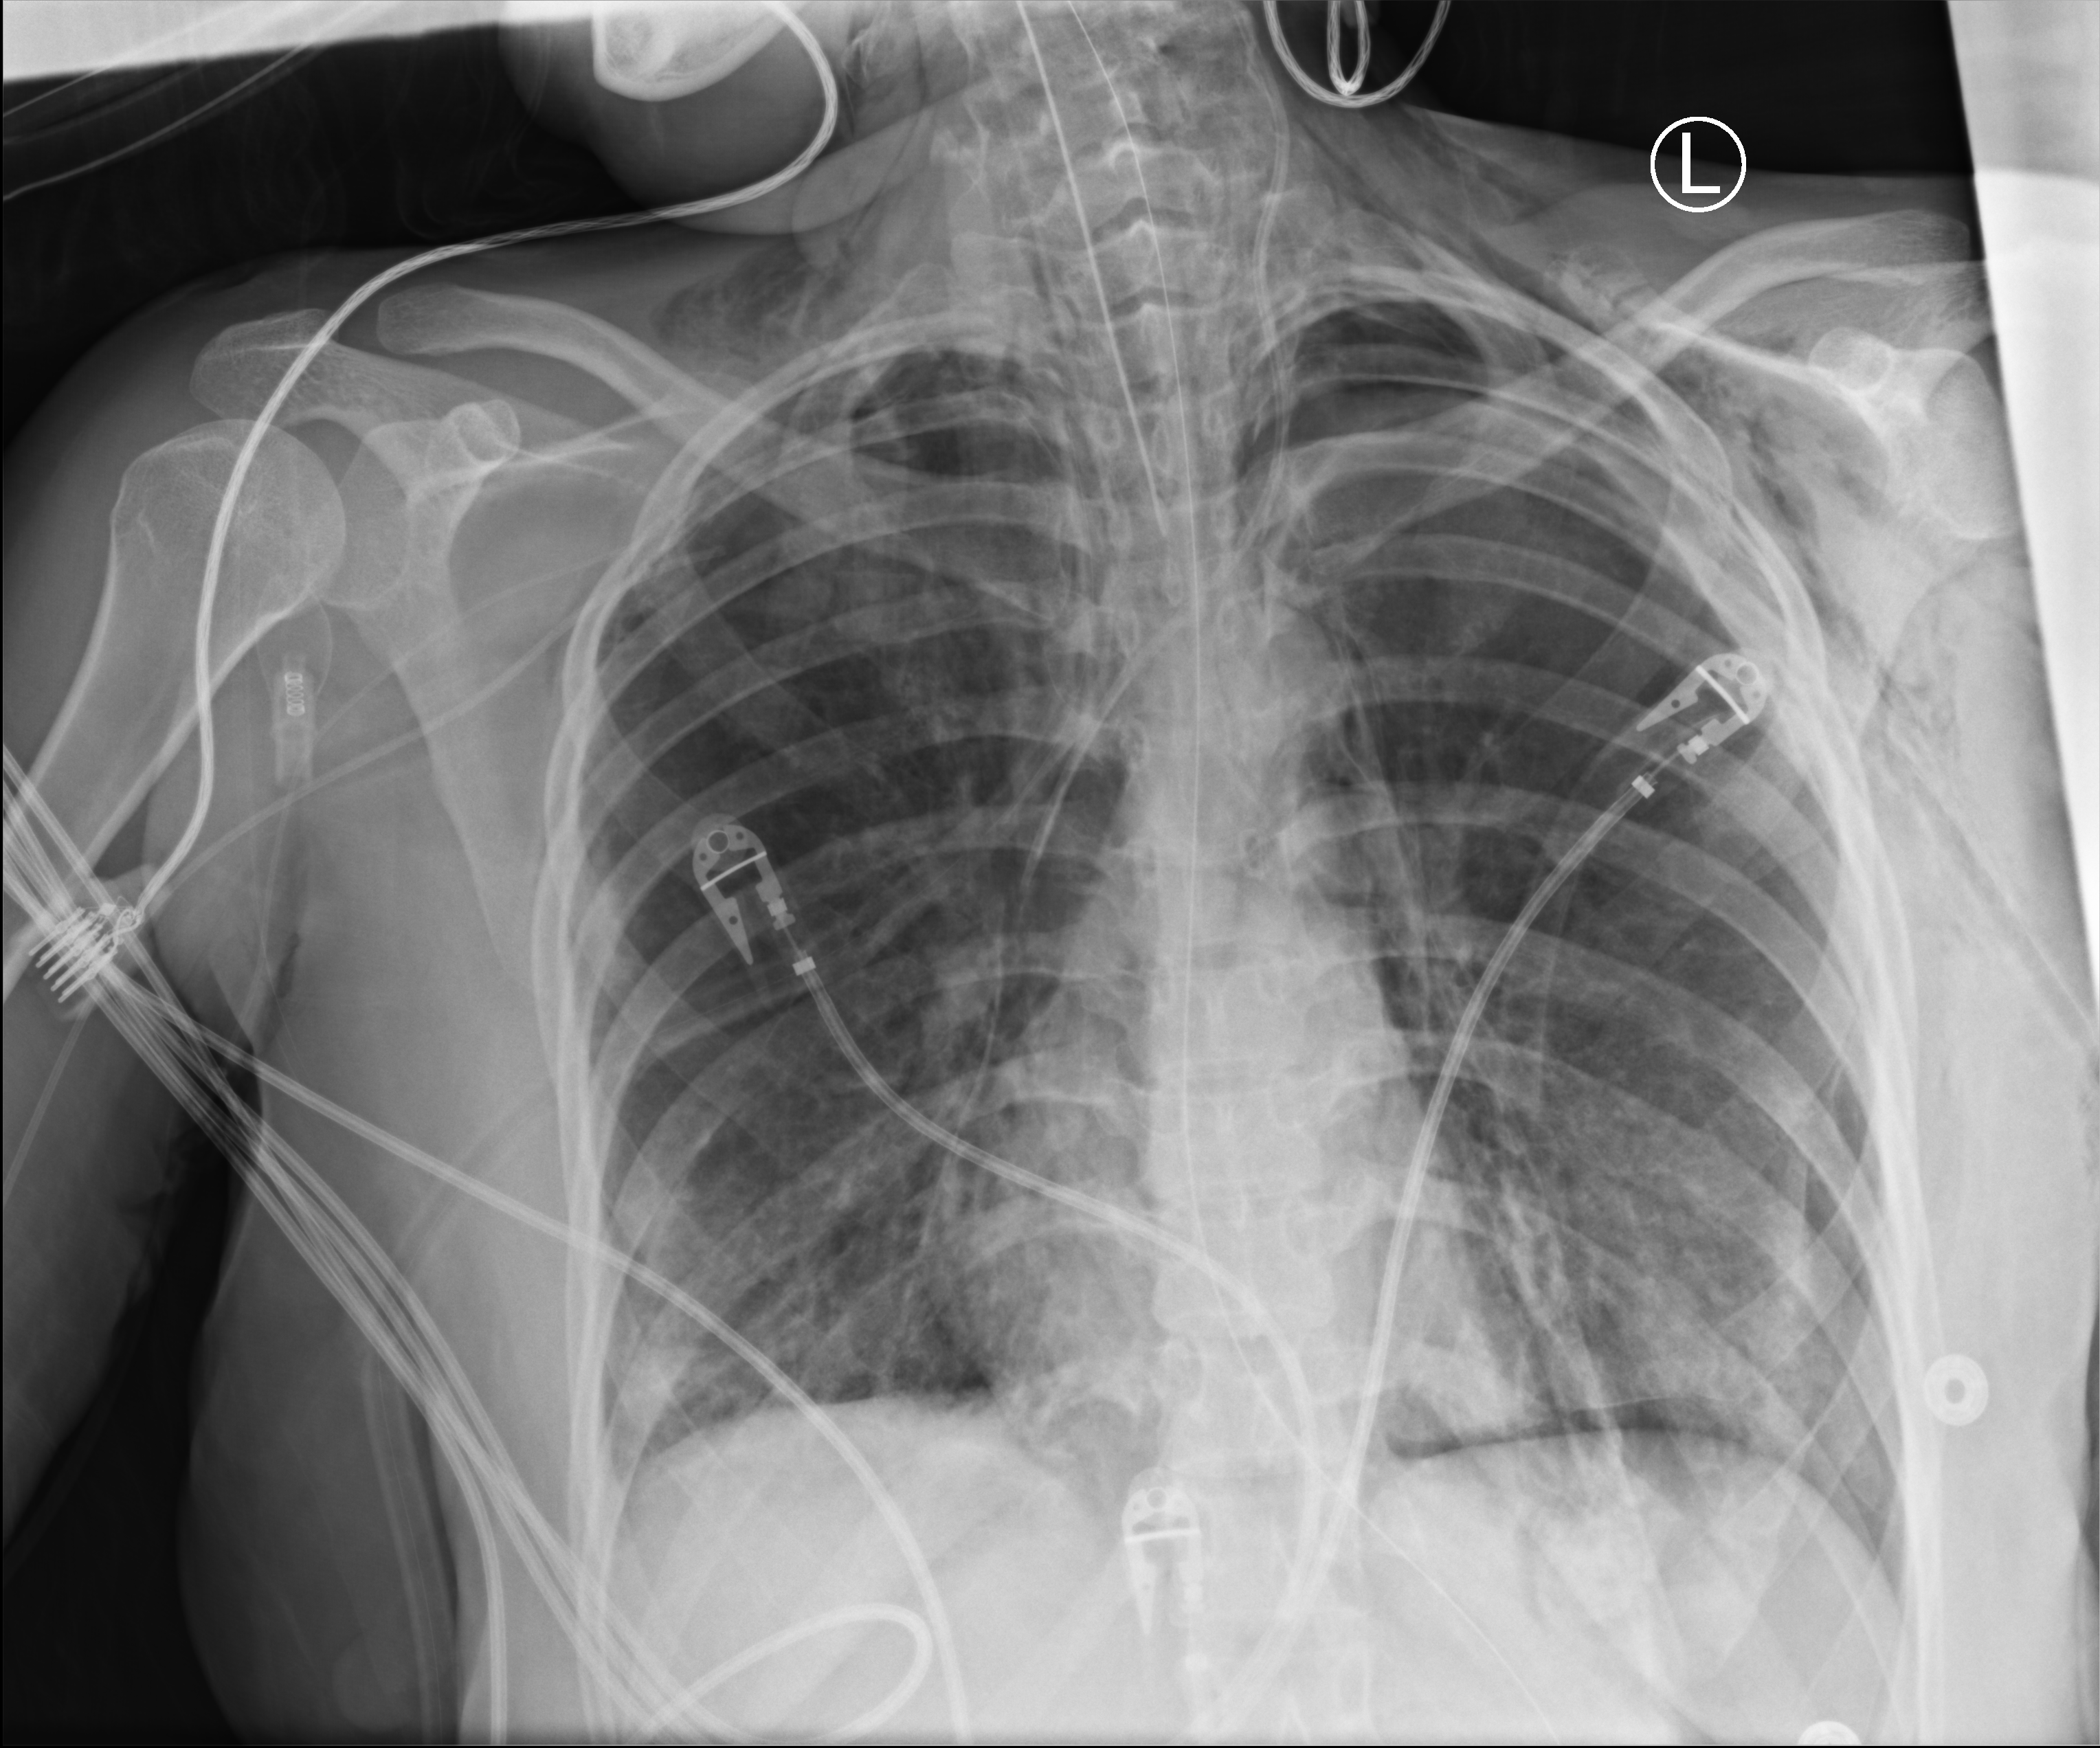
Bedside chest radiograph (computed radiography). Adult patient hospitalised with COVID-19, age 18–59 years.
From the hospital-stay record, not from the radiograph (when in the stay this image was taken is not recorded):
- chronic kidney disease (admission record): no
- admitted to intensive care during this hospital stay: yes
- mechanically ventilated during this hospital stay: yes